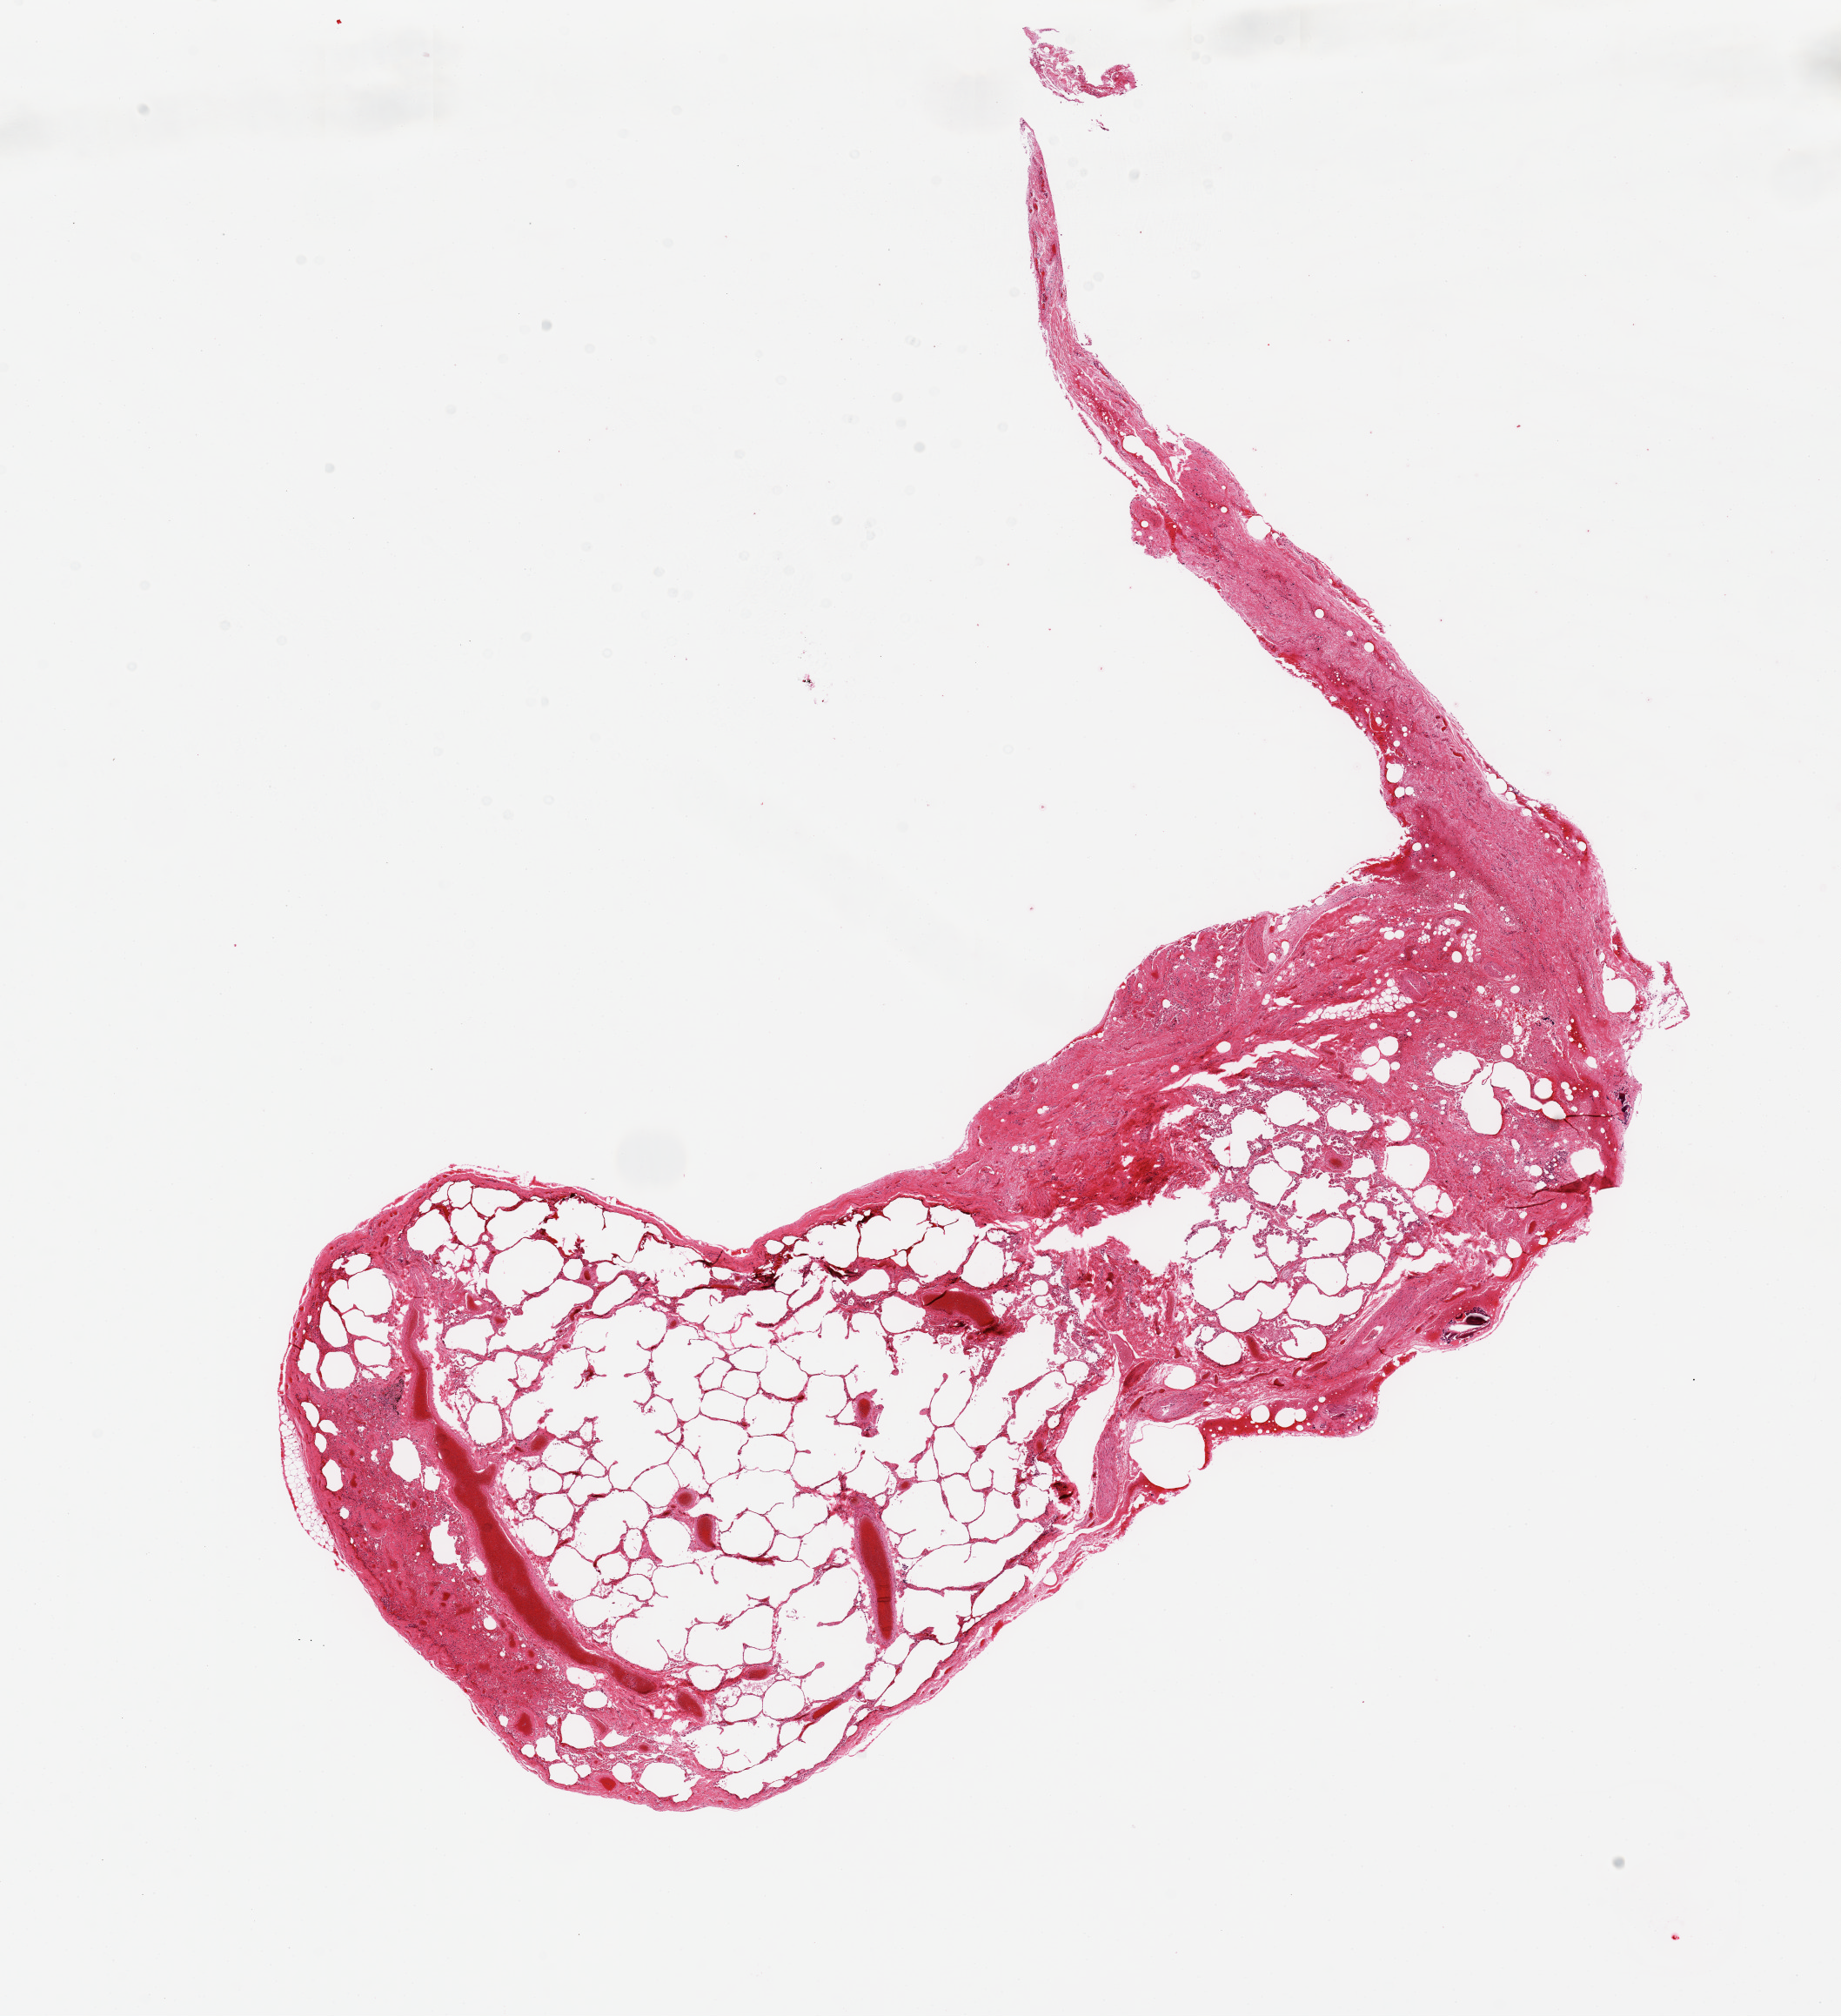
Digitized haematoxylin and eosin-stained section — a low-resolution overview of the entire scanned area, about 16.7 x 18.3 mm (slide scanned at 20x), PAXgene-fixed, paraffin-embedded tissue, section of lung (target tissue), tissue donor sample.
• reviewer comment on this tissue sample: 13x6 mm; Dilated alveoli, emphysema, fibrosis, probable pleural scar*(See Additional Comments below)(Attachment A)